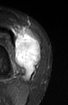
MRI of an extremity soft-tissue mass, one axial slice; slice 27 of 52 in the series (ordered by position); STIR; MR volume resampled by the dataset authors to the PET/CT grid (not the native acquisition matrix); 68 × 105 image matrix, field of view 66 × 103 mm. Female patient. Case-level facts recorded for this patient, not image findings: histological type: spindle cell suggestive of biphasic synovial sarcoma; grade: intermediate; site of the primary tumour: left knee.
Annotated regions visible in this slice (expert contour drawn on MRI and transferred to this co-registered scan by the dataset authors):
- gross tumour volume including surrounding oedema: bounding box <14,29,41,76> (left, top, right, bottom; pixels)
- gross tumour volume (mass): <14,31,41,76>